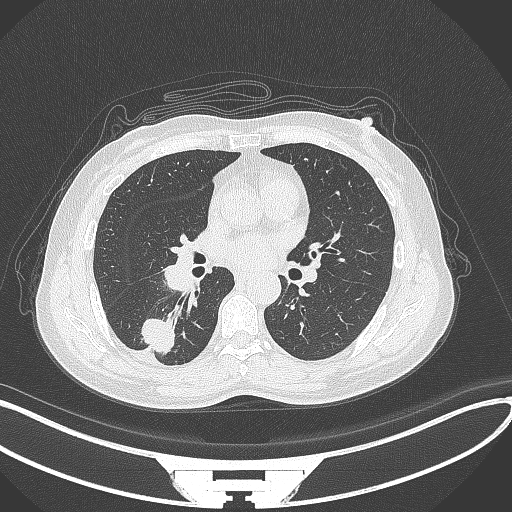
Chest CT, one axial slice. Reconstruction kernel B70f. Lung window (W 1500 / L -600 HU). 1 mm slice thickness. 512 × 512 image matrix, field of view 400 × 400 mm. Female patient, age 55 years. Case-level facts recorded for this patient, not image findings: clinical TNM (as recorded): T1c N1 M0.
Structures marked on this image (rectangle marked by the reading radiologist):
- lung tumour (recorded histology: adenocarcinoma): bounding box (x1, y1, x2, y2) in pixels: (137, 318, 180, 356)